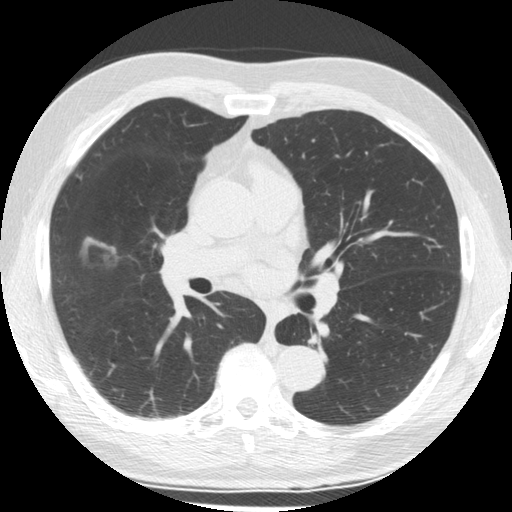
Low-dose screening chest CT, axial slice, first (baseline) screen, lung window (W 1500 / L -600 HU), 2.5 mm slice thickness, standard (soft-tissue) reconstruction kernel (STANDARD), slice 74 of 176 in the series, 512 × 512 image matrix. Male participant, aged 64 years at enrolment. Former smoker at enrolment.
Expert reader's lesion annotation, bounding box [x1, y1, x2, y2] px = [69, 220, 130, 285]. The screening reader recorded 2 non-calcified nodules or masses ≥4 mm on this exam (right middle lobe, left lower lobe); which of them this box marks is not recorded. Official screen result: positive, change unspecified: nodule(s) >= 4 mm or enlarging nodule(s), mass(es), or other non-specific abnormalities suspicious for lung cancer. Participant outcome: lung cancer diagnosed 58 days after this screen — papillary adenocarcinoma, NOS, right middle lobe, well differentiated (G1), stage IA (AJCC 6th edition), 25 mm at pathology.